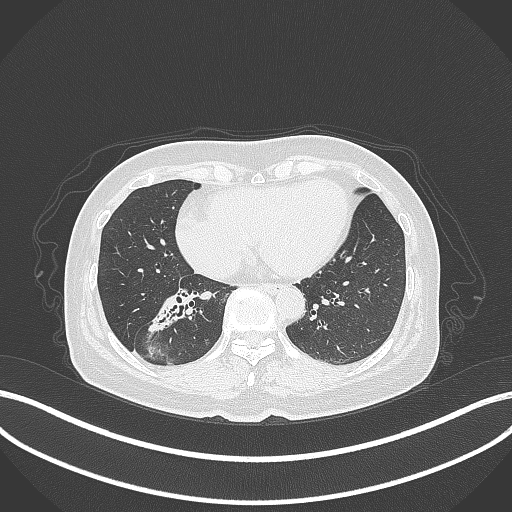
Chest CT, one axial slice; slice 143 of 429 in the series (ordered by position); reconstruction kernel B70f; 120 kVp; lung window (W 1500 / L -600 HU); 512 × 512 image matrix, field of view 400 × 400 mm. Female patient, age 67 years. Case-level facts recorded for this patient, not image findings: clinical TNM (as recorded): T1c N1 M0.
Outlined on this slice (bounding box drawn by a radiologist):
- lung tumour (recorded histology: adenocarcinoma): box from (x=142, y=292) to (x=198, y=329) px